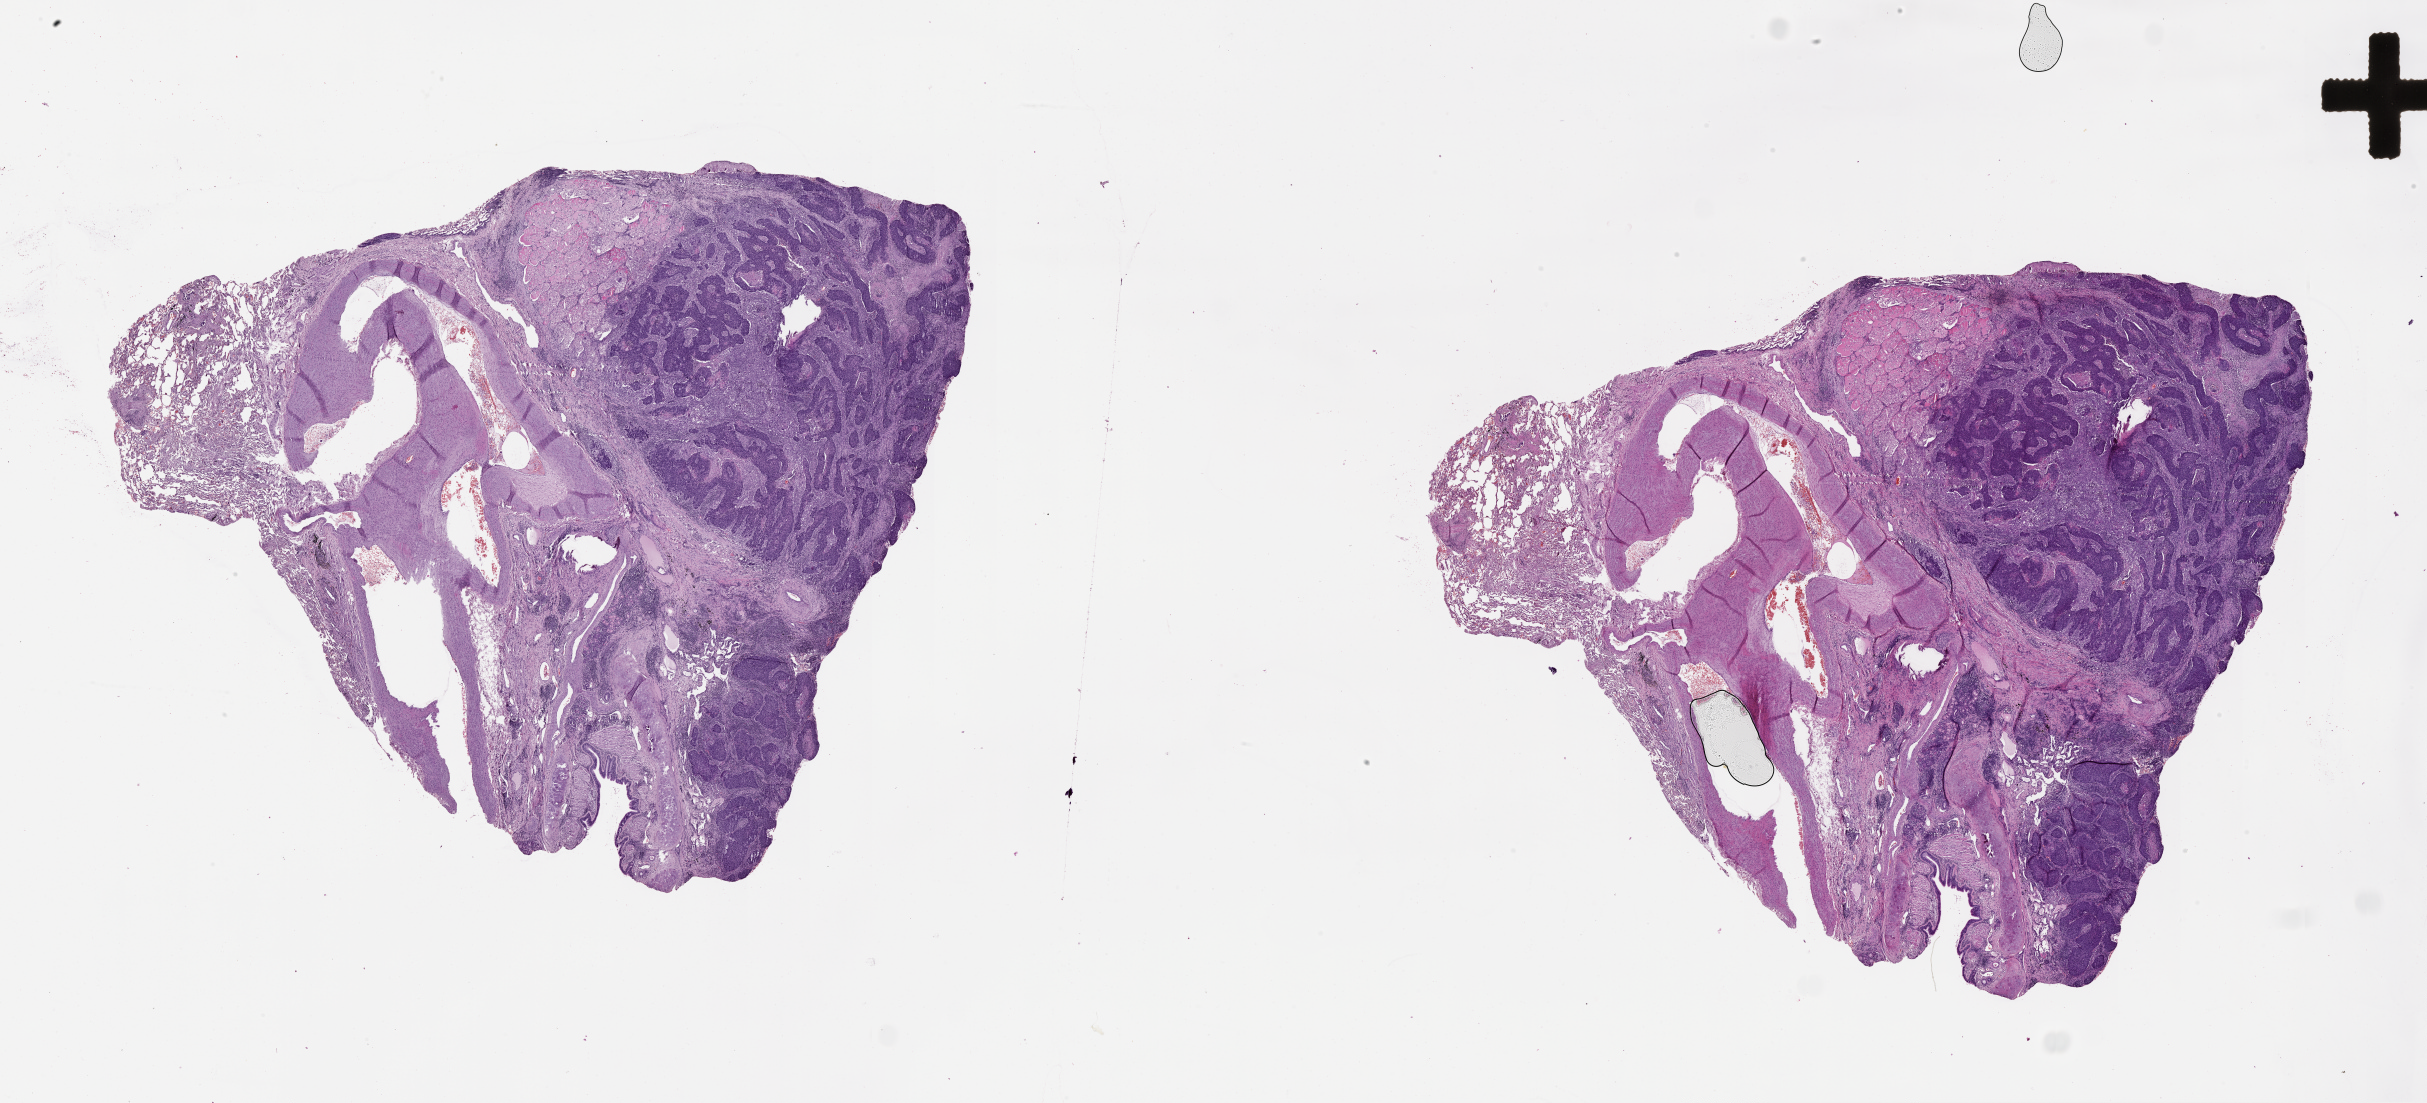
Whole-slide histology image, Hematoxylin and eosin (H&E) stained — whole scanned area (about 39.1 x 17.8 mm) shown as a low-resolution overview, tumour tissue sample, lung. 62-year-old female patient.
Patient diagnosis (cohort enrolment): squamous cell carcinoma (lung).